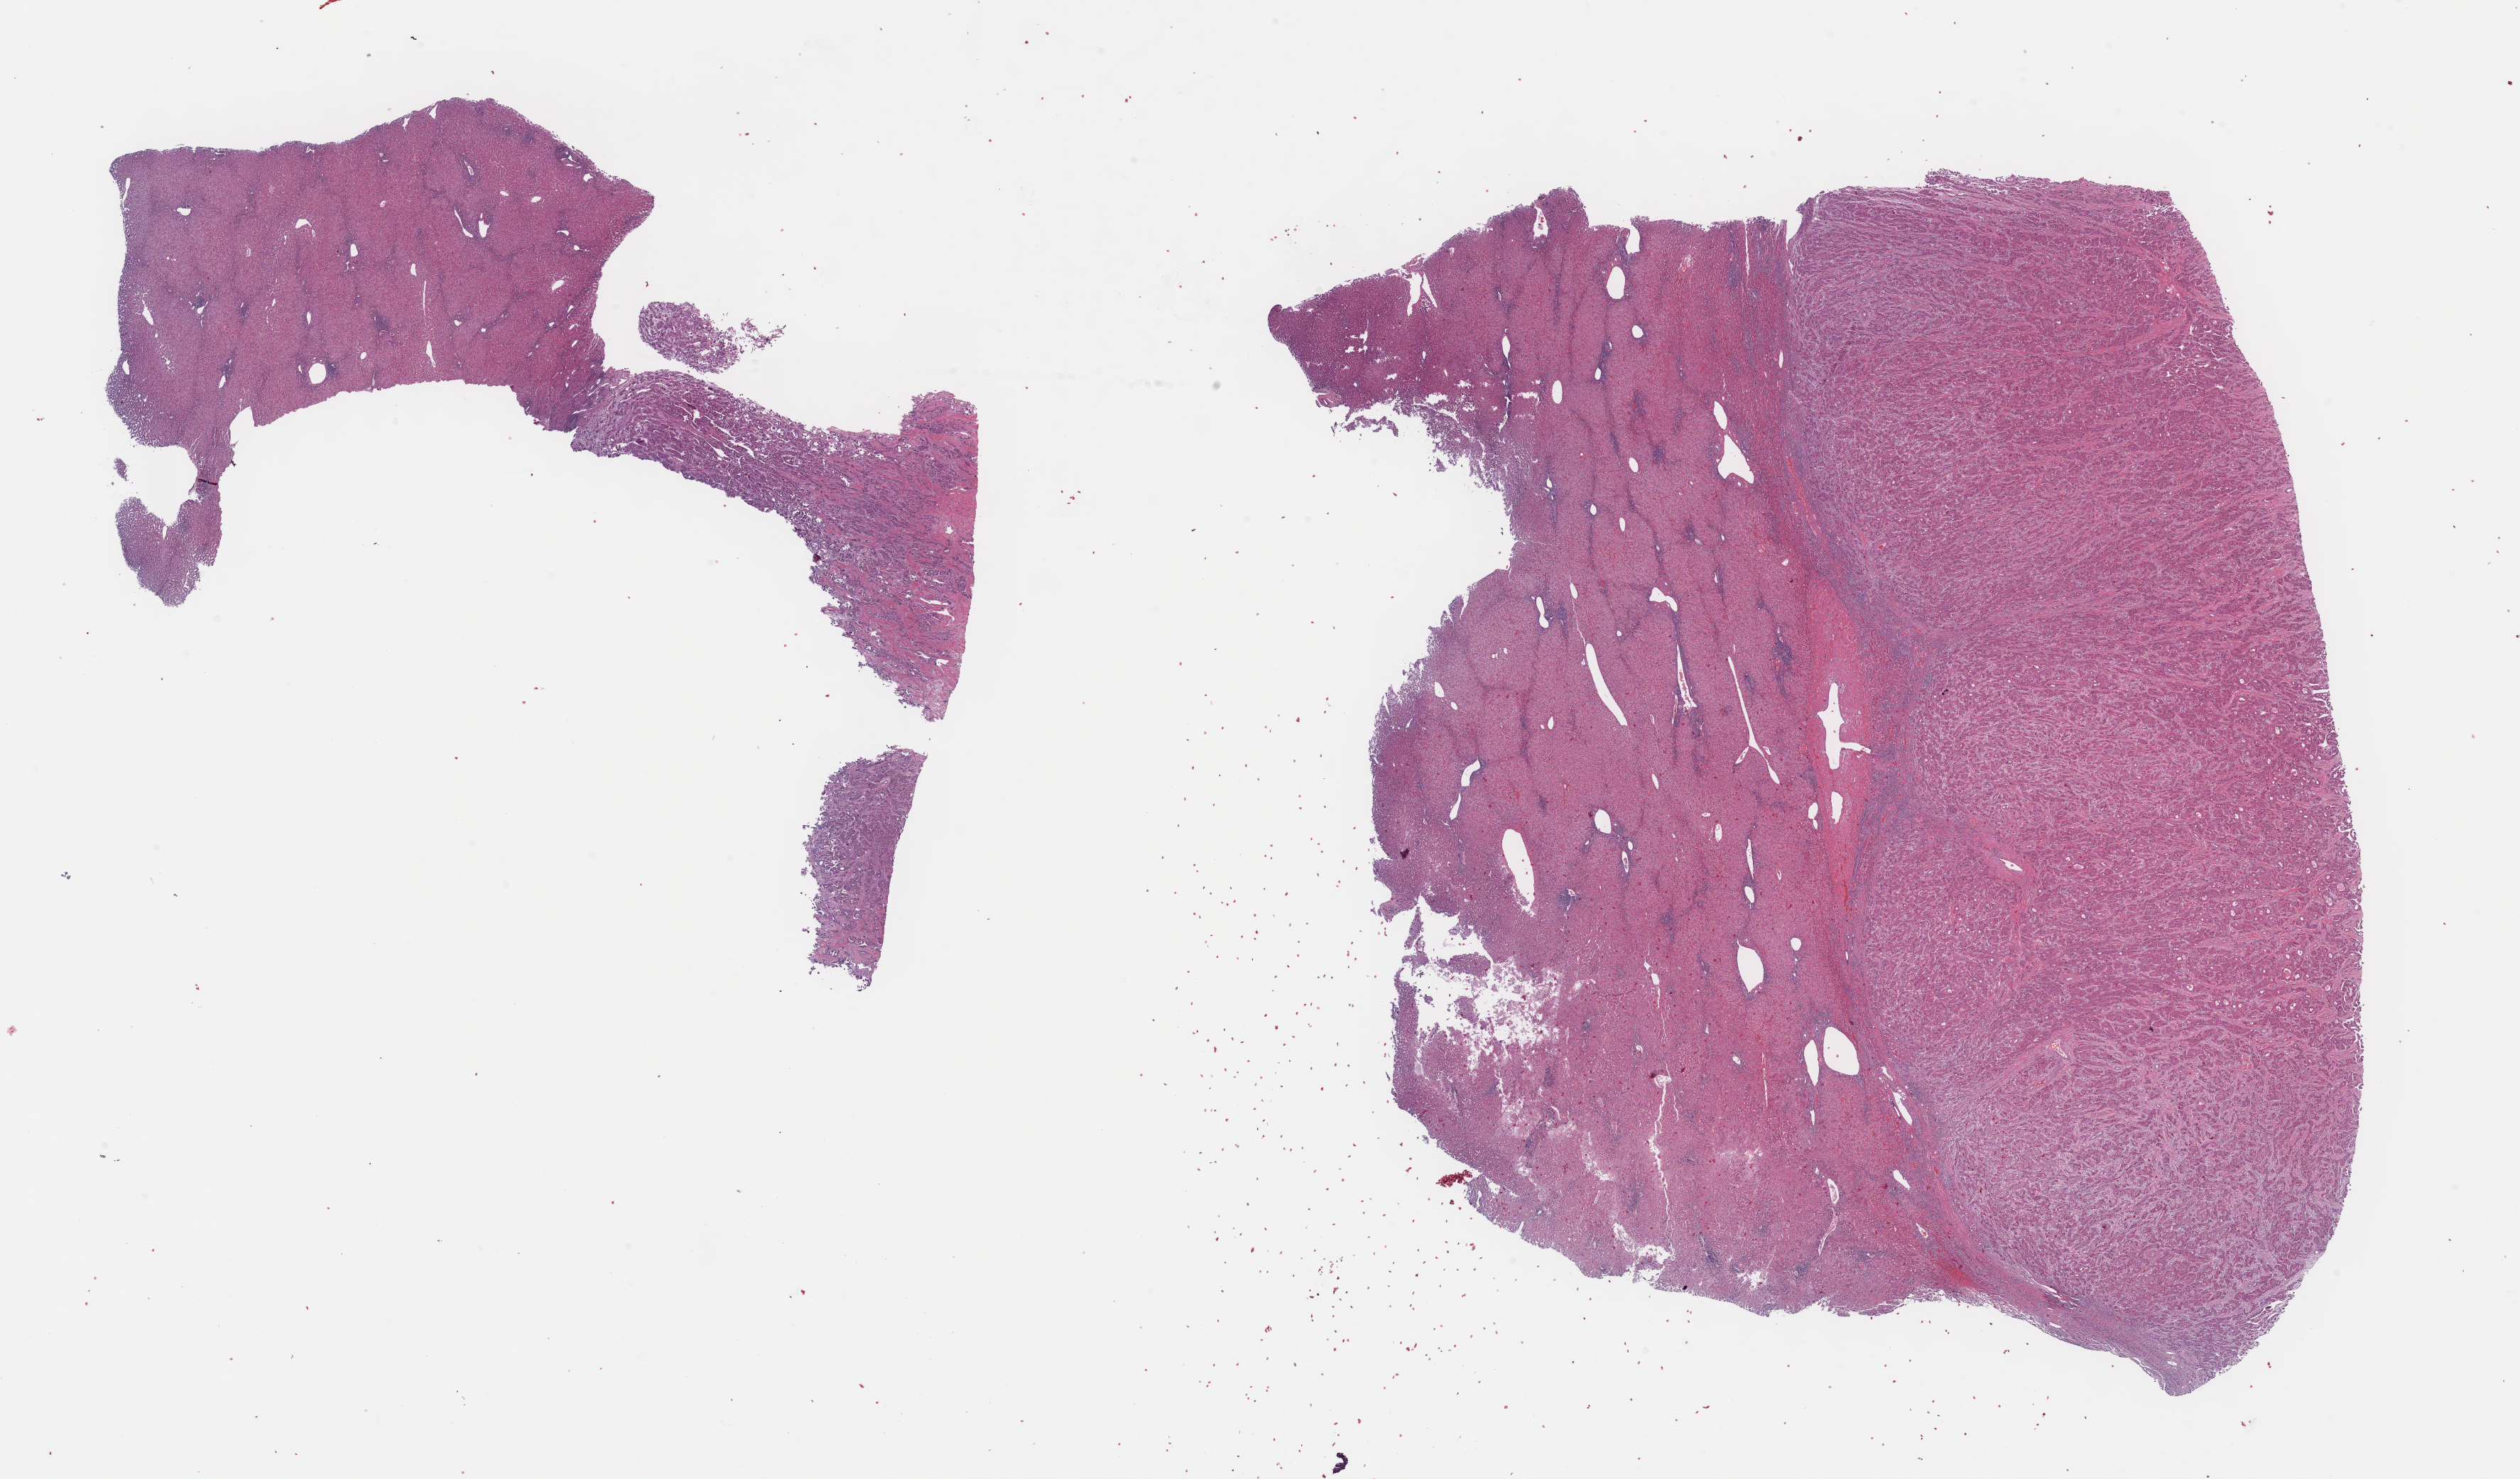
Whole-slide histology image, Hematoxylin and eosin (H&E) stained — a low-resolution overview of the entire scanned area, about 28.7 x 16.8 mm (slide scanned at 40x). Formalin-fixed paraffin-embedded (FFPE) diagnostic section. Primary tumour sample from the liver. Male patient; age at initial diagnosis 25 years. Histologic grade: G2 (moderately differentiated).
* histologic diagnosis: Hepatocellular carcinoma, fibrolamellar
* AJCC pathologic stage: I (7th edition)